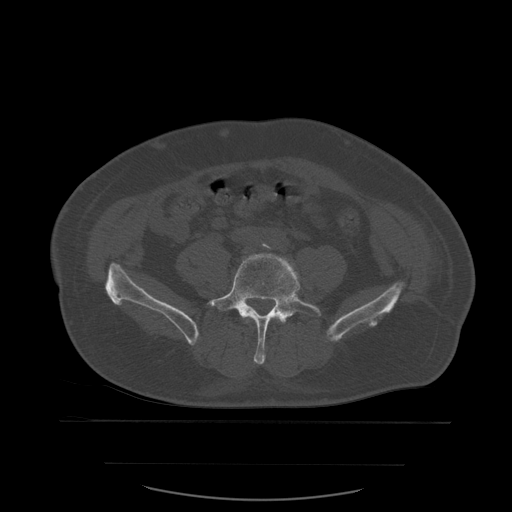
CT including the spine, one axial slice; position 142 of 590 along the scan axis; bone window (W 1800 / L 400 HU); 1.25 mm slice thickness; 512 × 512 image matrix, field of view 479 × 479 mm. Patient age 71 years. Case-level facts recorded for this patient, not image findings: primary cancer: lung.
Outlined on this slice (semi-automatically segmented with operator editing):
- L4 vertebra: box from (x=247, y=316) to (x=280, y=323) px
- L5 vertebra: (x=207, y=253)–(x=322, y=365)